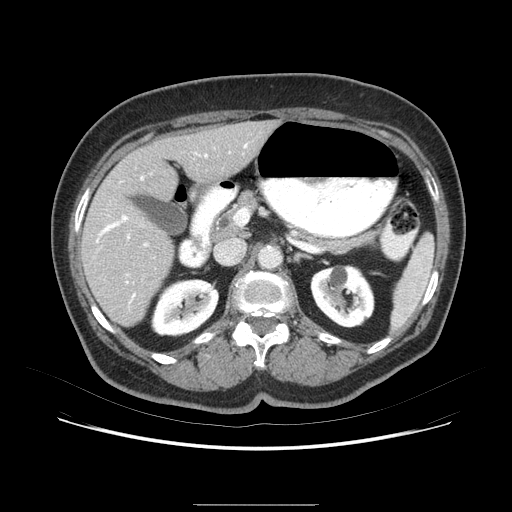
Contrast-enhanced abdominal CT (liver protocol), one axial slice. Slice 38 of 79 in the series (ordered by position). 120 kVp. Soft-tissue window (W 400 / L 40 HU). 512 × 512 image matrix, field of view 380 × 380 mm. From the clinical record (not read from this slice): diagnosis: hepatocellular carcinoma (patient treated with transarterial chemoembolisation; whether this scan precedes or follows treatment is not stated here); TNM stage (as recorded): Stage-I; Child-Pugh class: A; tumour nodularity: uninodular.
Annotated regions visible in this slice (semi-automatic segmentation, software-assisted and operator-edited):
- liver parenchyma outside the tumour (the mass and vessels are separate outlines, so this box may not span the whole liver): bounding box [x1, y1, x2, y2] px = [78, 120, 284, 334]
- mass: [124, 202, 164, 248]
- liver vessels: [113, 136, 262, 310]